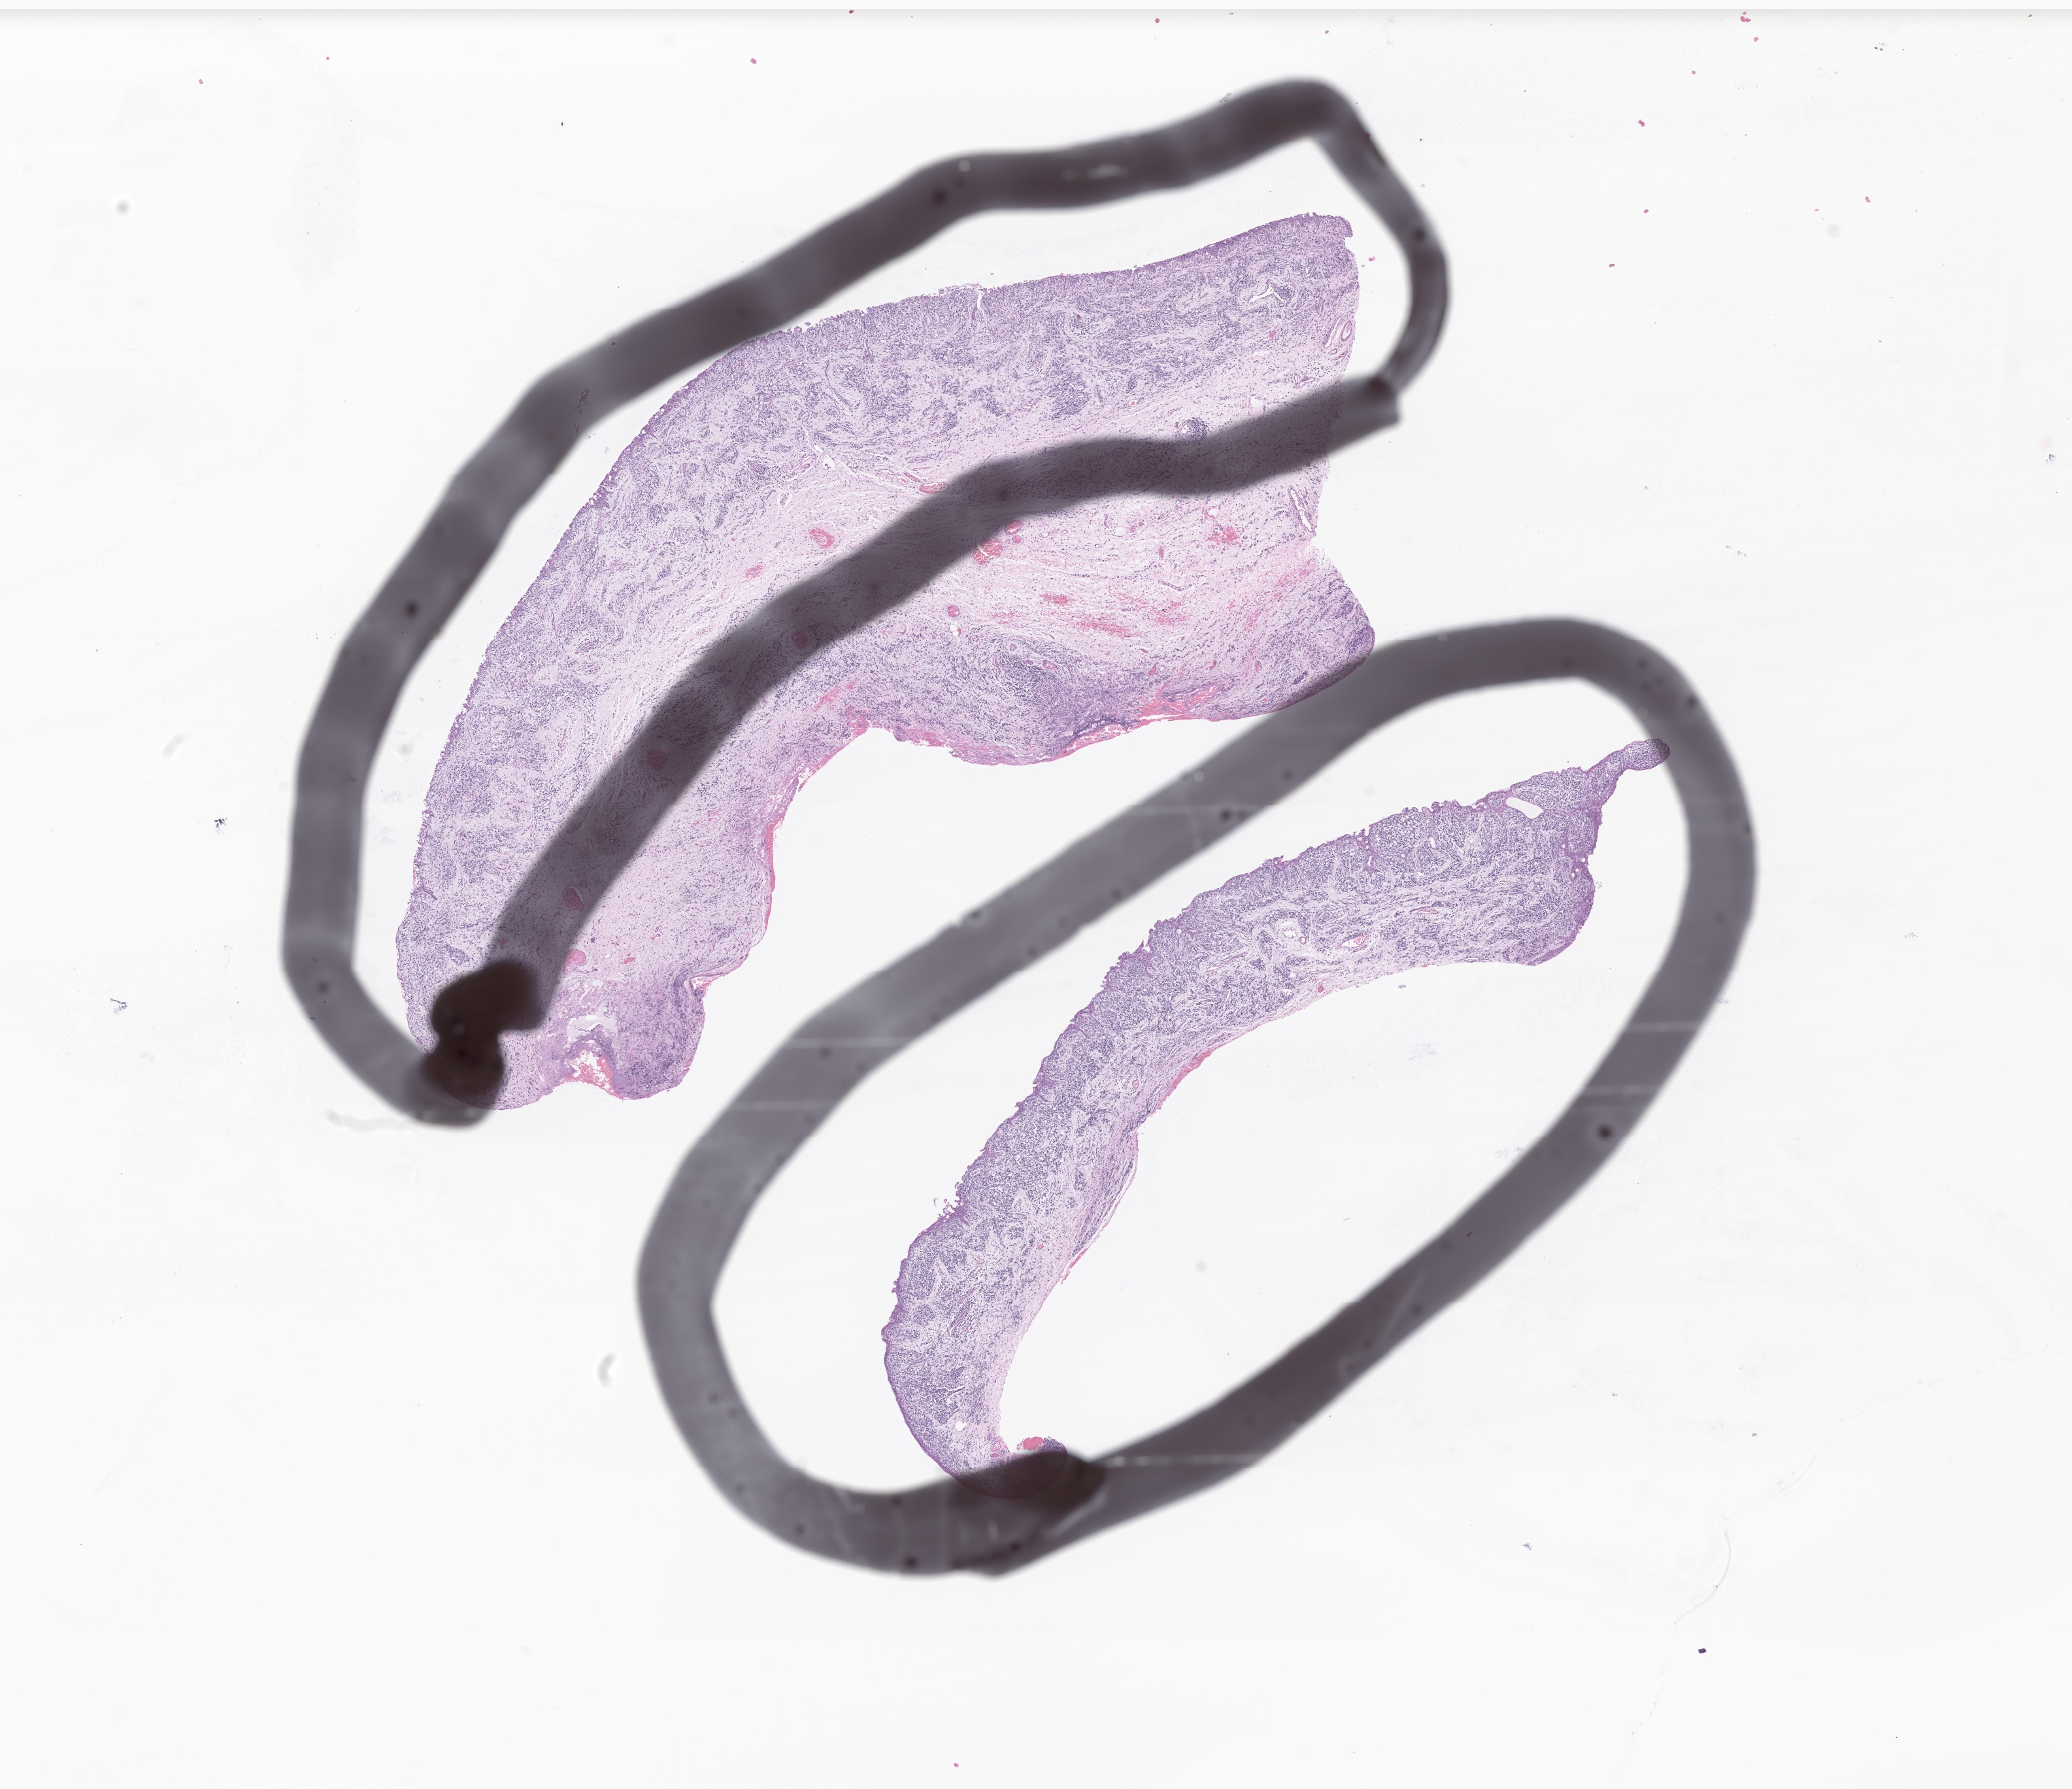
Digitized H&E-stained section of tumor tissue from the orbit — low-resolution overview of the scanned area, about 13.4 x 11.5 mm; formalin-fixed, paraffin-embedded (FFPE) tissue. Female patient, age 46 months (3 years 10 months).
Diagnosis (ICD-O-3 morphology term): Embryonal rhabdomyosarcoma, NOS.